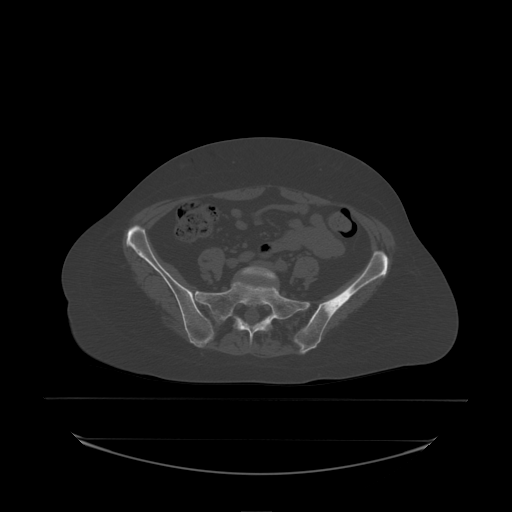
CT including the spine, one axial slice; slice 31 of 242 in the series (ordered by position); bone window (W 1800 / L 400 HU); 512 × 512 image matrix, field of view 500 × 500 mm. Patient: female, 53 years. From the clinical record (not read from this slice): primary cancer: lung; vertebrae with lytic lesions (as recorded): T7, L1.
Structures marked on this image (semi-automatically segmented with operator editing):
- L5 vertebra: bounding box [x1, y1, x2, y2] px = [242, 267, 277, 288]